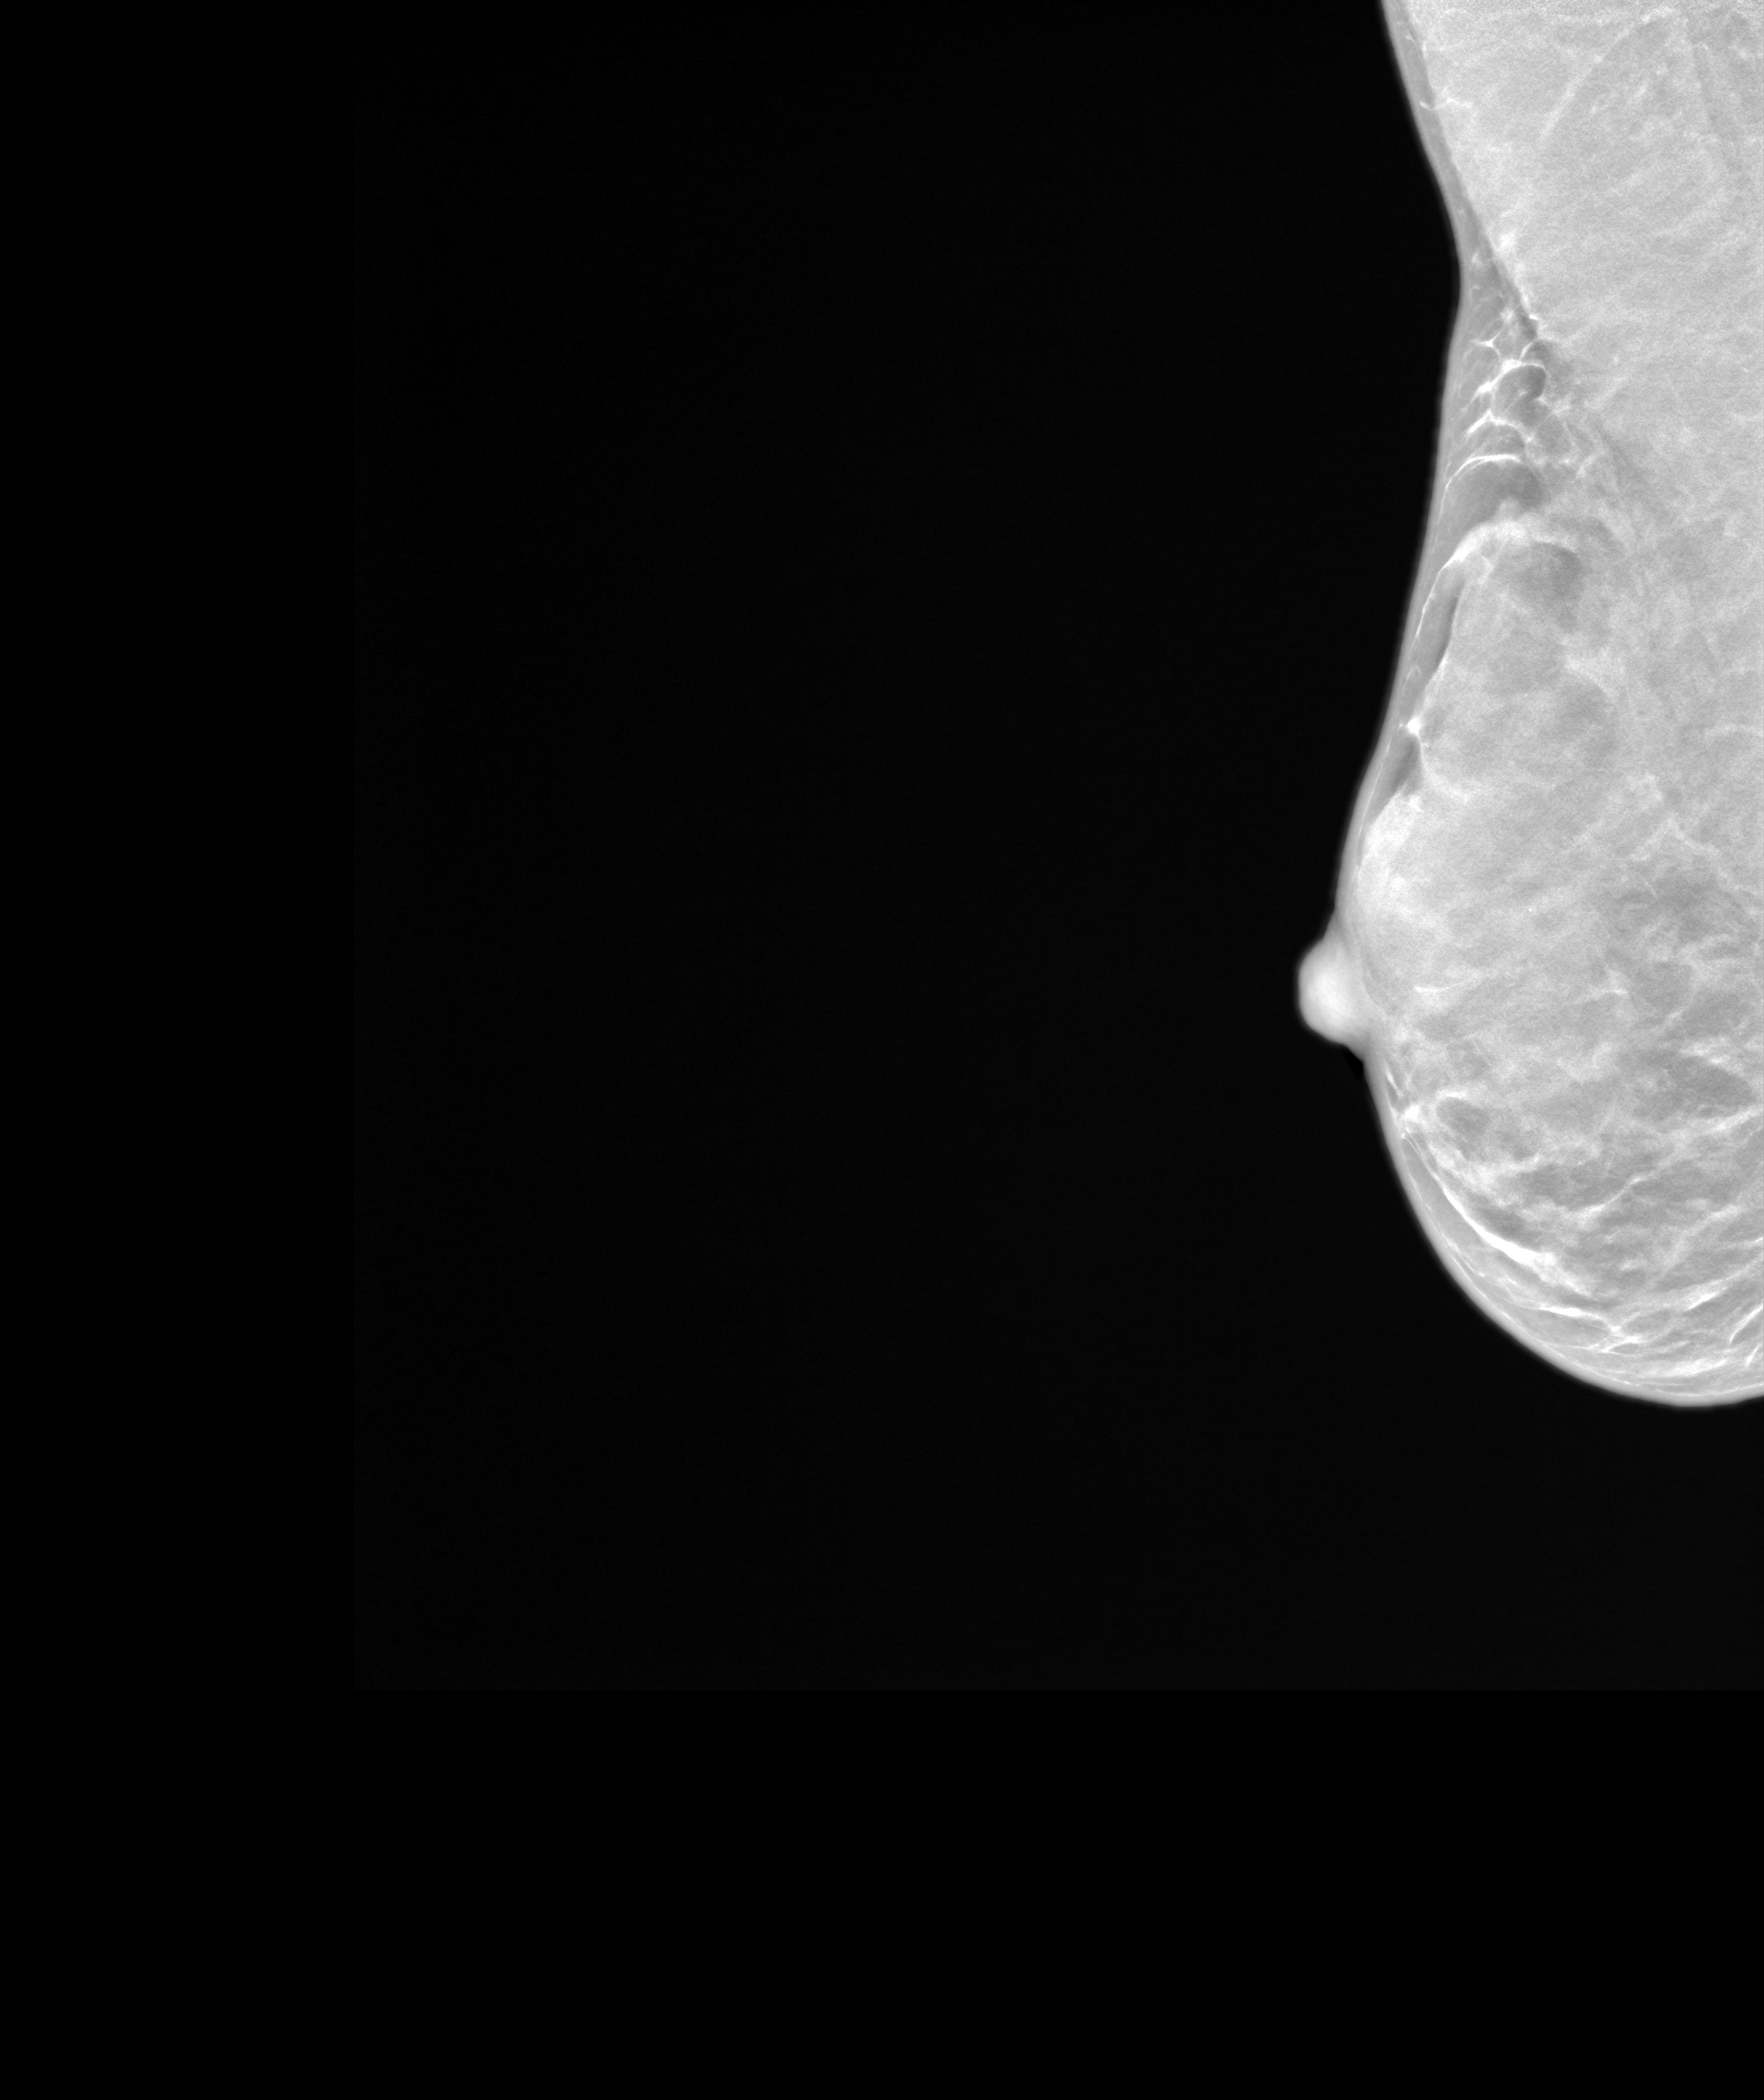
Synthetic 2-D view generated from a tomosynthesis acquisition (not an FFDM exposure), right breast, MLO view, annual screening mammography examination, system: SenoIris_1SP1.1(421). Patient aged 54 years (female).
- breast density at the screening exam (both breasts): extremely dense (BI-RADS density category d)
- final BI-RADS category for the screening round (tomosynthesis exam, both breasts): category 1
- recall: no recall after this screen